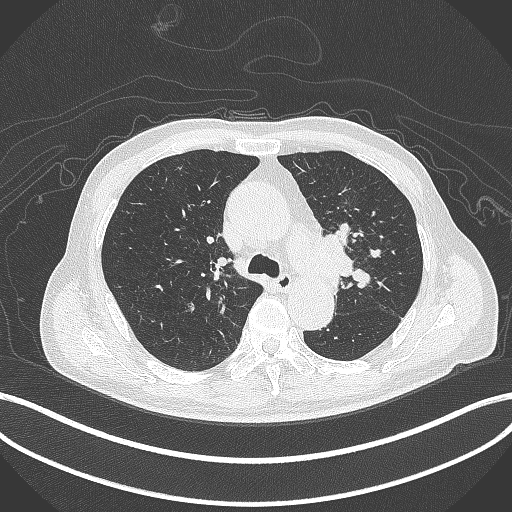
Chest CT, one axial slice. Position 294 of 417 along the scan axis. Reconstruction kernel B70f. Lung window (W 1500 / L -600 HU). 512 × 512 image matrix, field of view 400 × 400 mm. Male patient, age 77 years. Case-level facts recorded for this patient, not image findings: clinical TNM (as recorded): T3 N1 M0.
Annotated regions visible in this slice (bounding box drawn by a radiologist):
- lung tumour (recorded histology: adenocarcinoma): box from (x=318, y=230) to (x=361, y=288) px